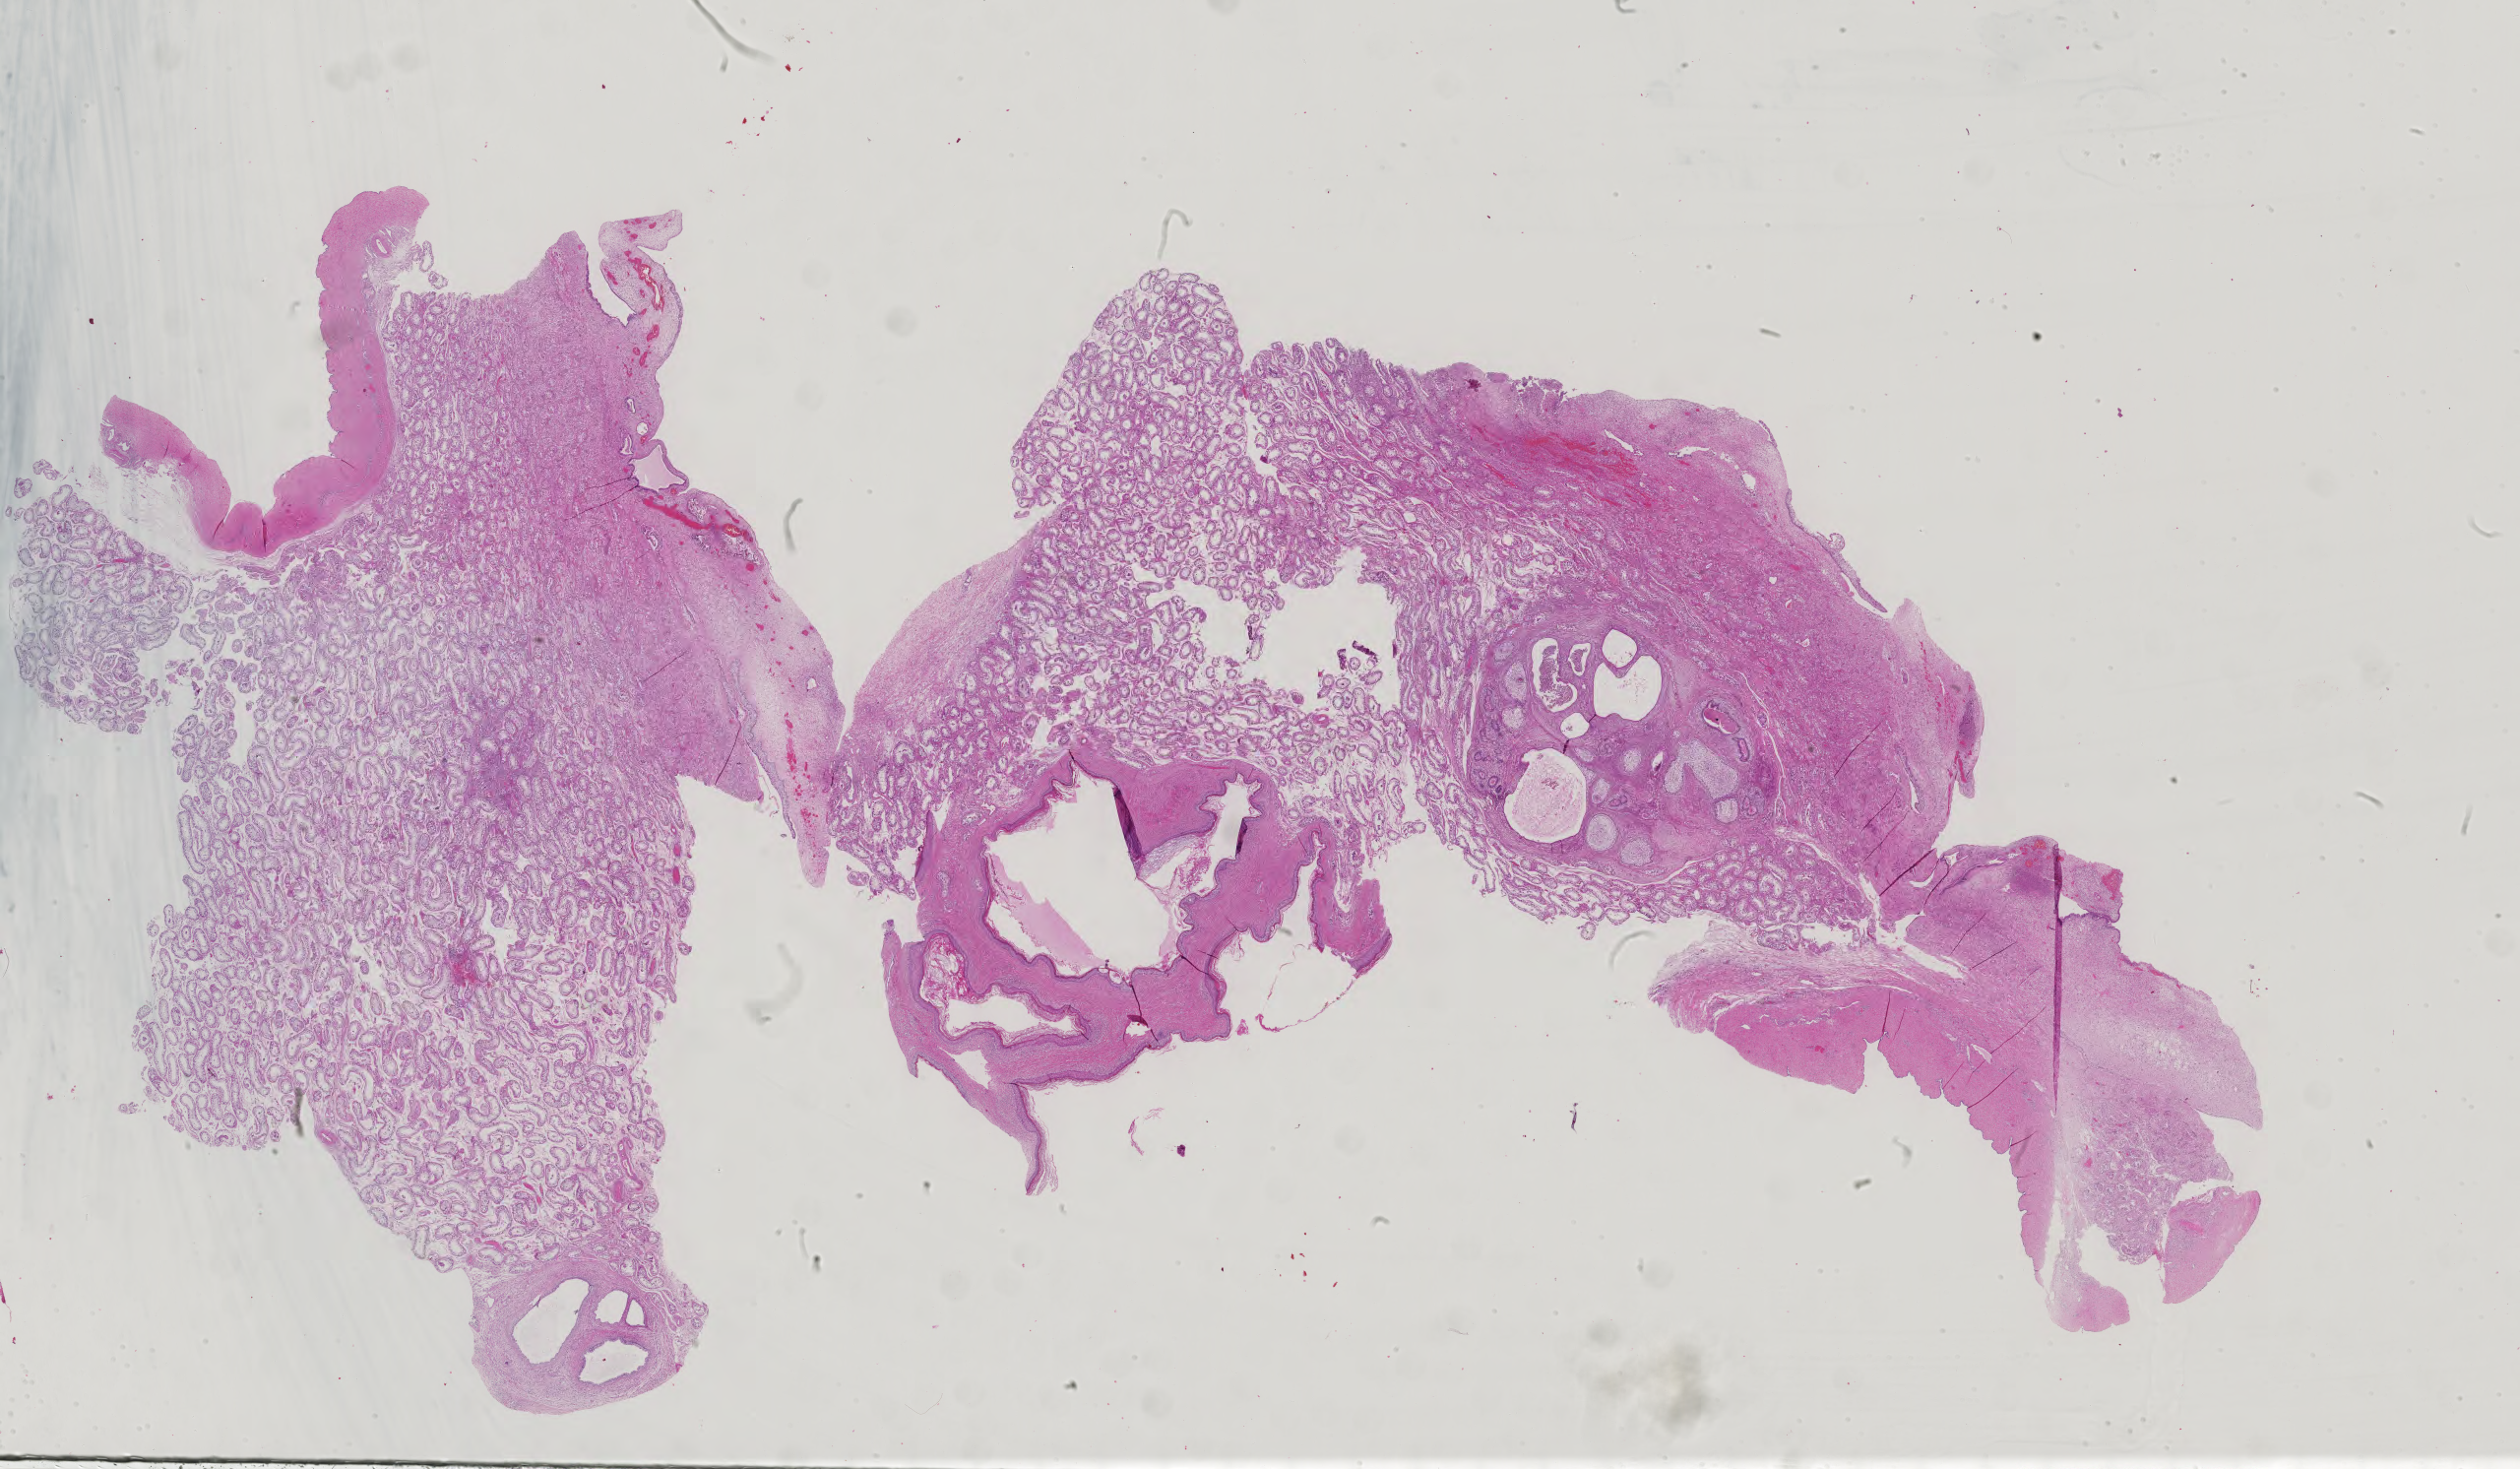
H&E-stained whole-slide image, low-resolution overview of the scanned area, about 37.3 x 21.7 mm (slide scanned at 40x). Male patient.
Specimen: FFPE section; primary tumour sample from the testis.